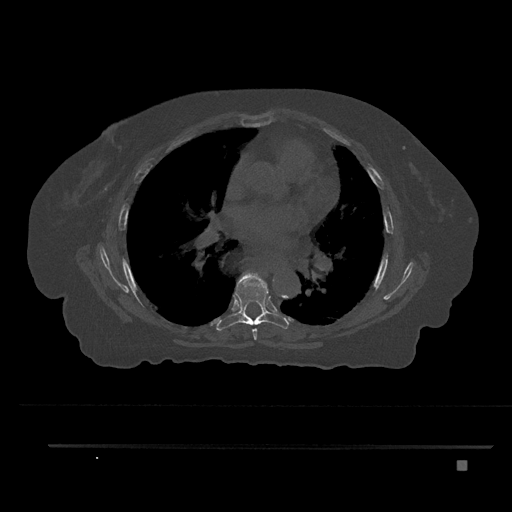
CT including the spine, one axial slice; position 496 of 797 along the scan axis; reconstruction kernel Br40s/3; bone window (W 1800 / L 400 HU); 0.5 mm slice thickness; 512 × 512 image matrix, field of view 437 × 437 mm. Patient: female, 76 years. From the clinical record (not read from this slice): primary cancer: lung; vertebrae with lytic lesions (as recorded): T11, L3.
Structures marked on this image (semi-automatic segmentation, software-assisted and operator-edited):
- T6 vertebra: box from (x=245, y=273) to (x=263, y=340) px
- T7 vertebra: (x=216, y=274)–(x=290, y=331)